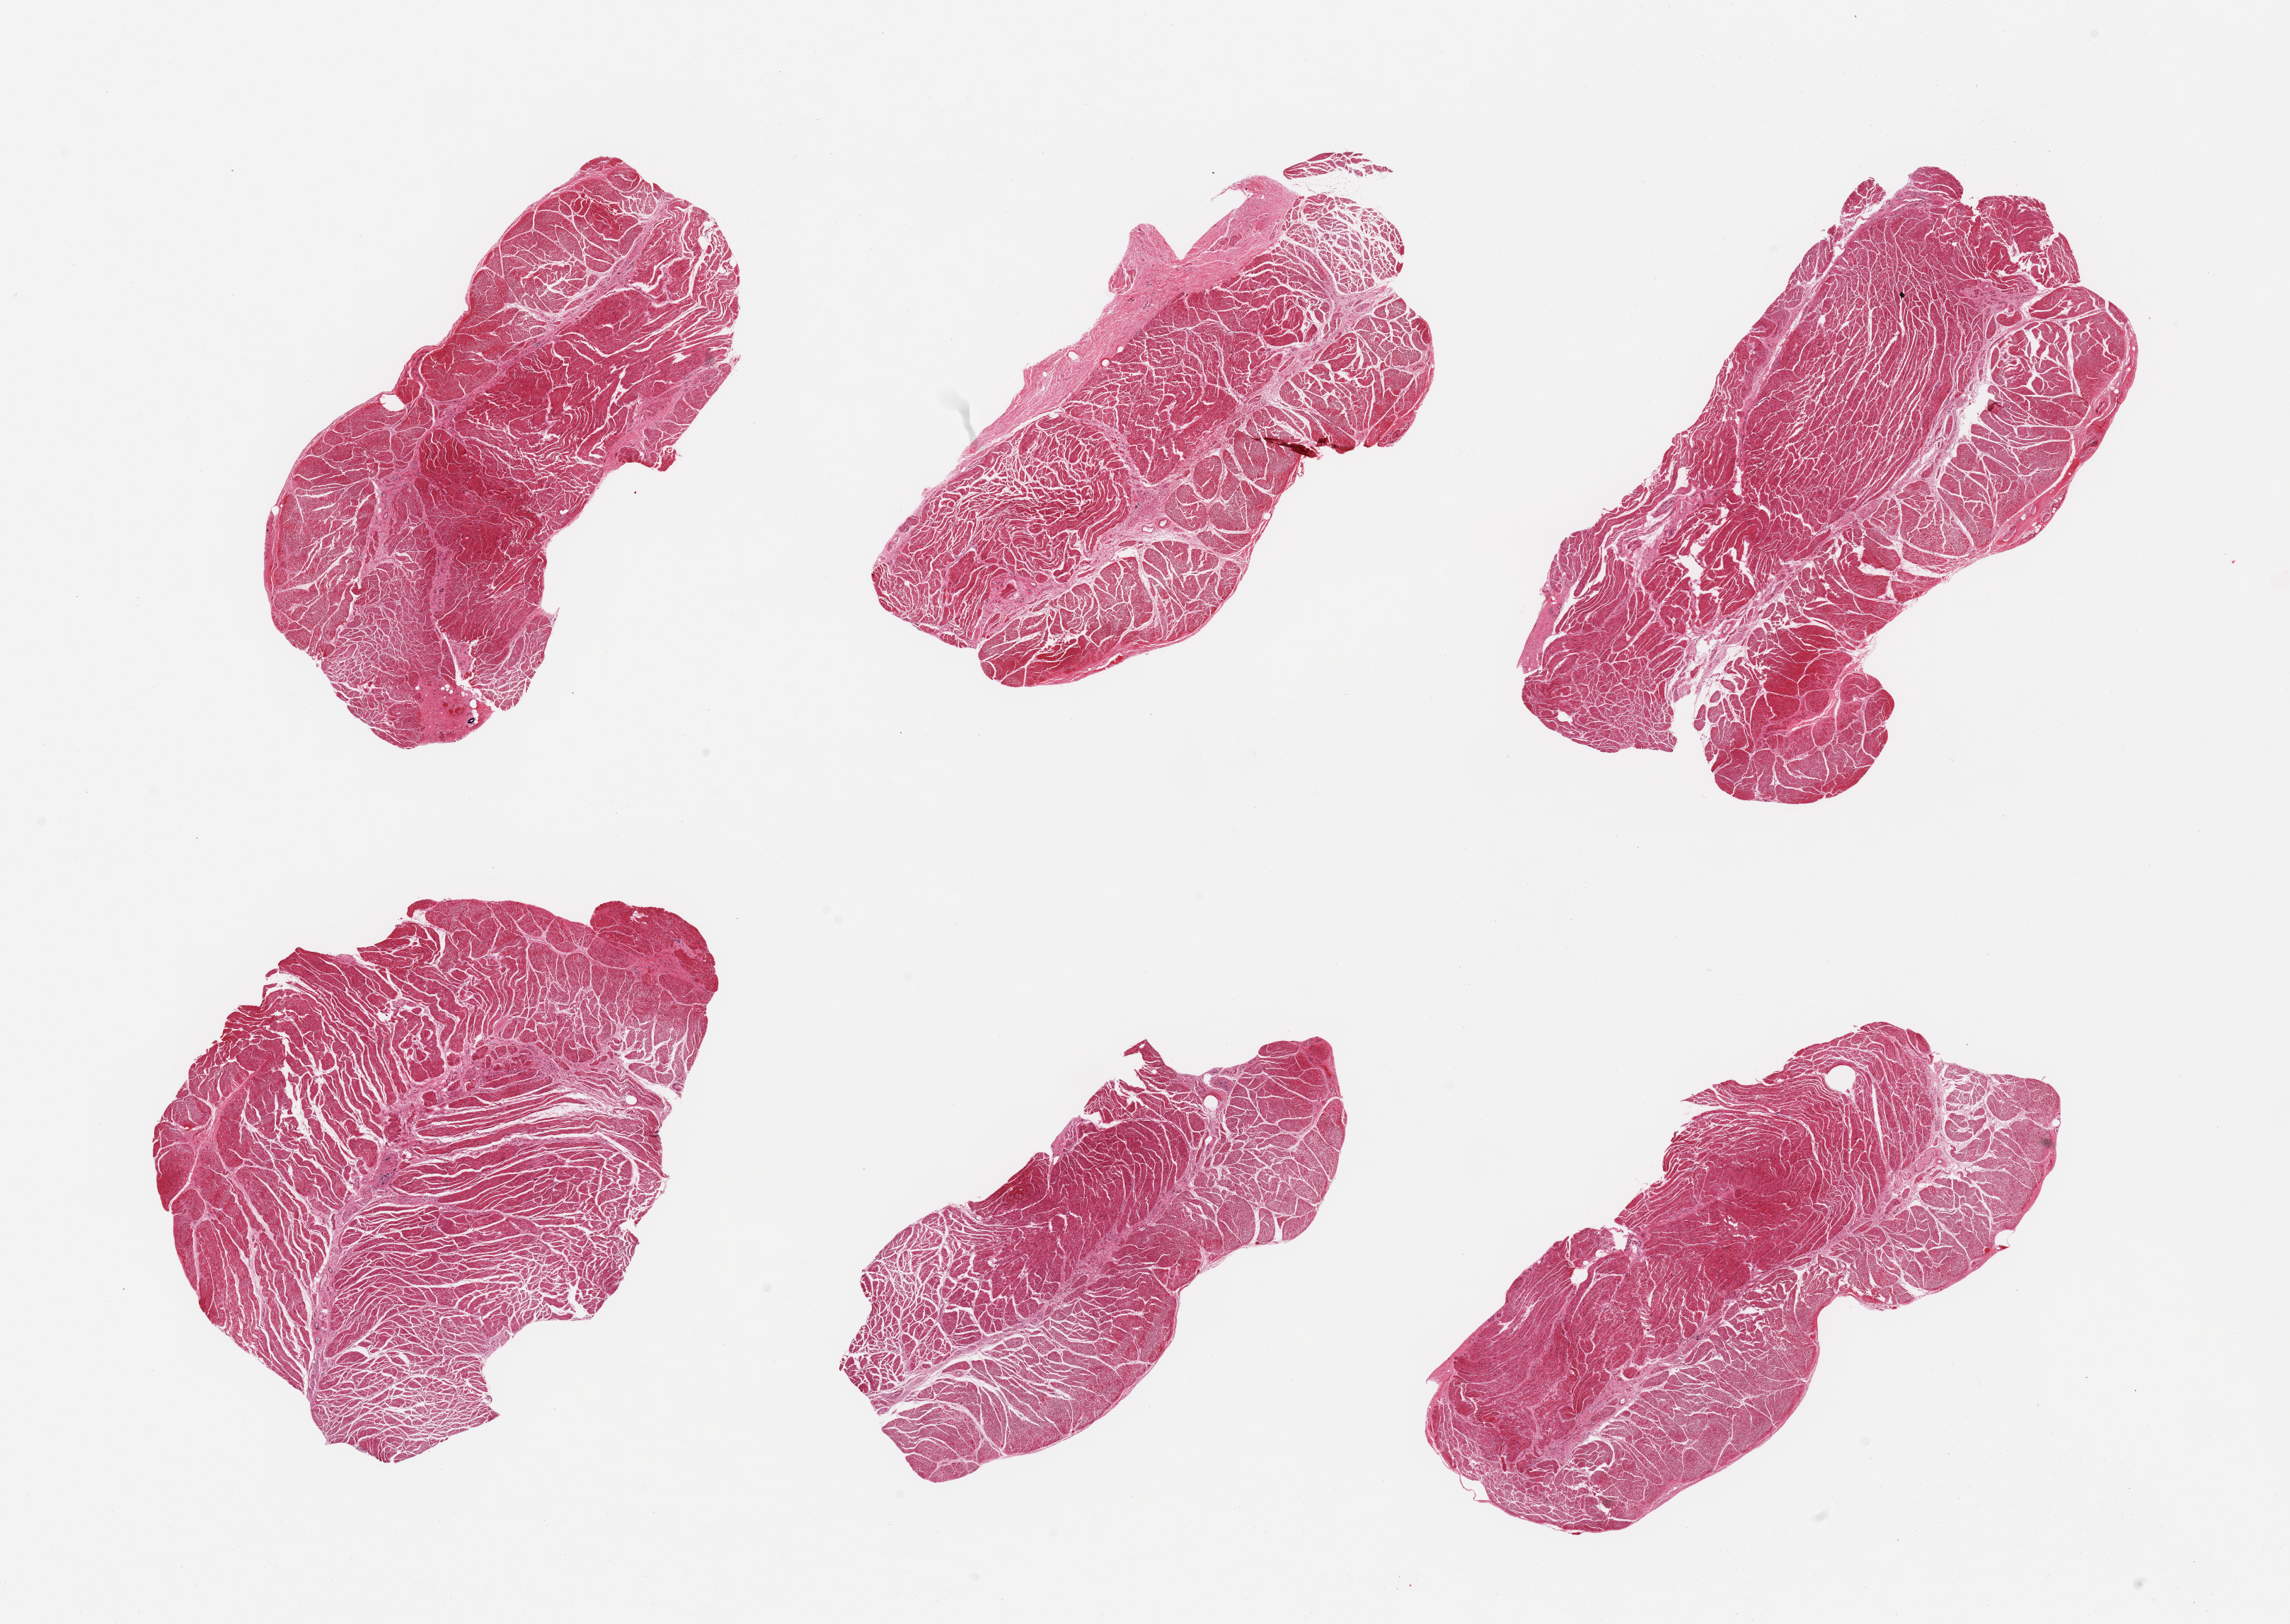
H&E whole-slide image, brightfield, a low-resolution overview of the entire scanned area, about 25.6 x 18.2 mm (from a 20x scan). PAXgene-fixed, paraffin-embedded tissue. Target tissue: gastroesophageal junction. Donor tissue sample. Male donor.
Pathologist's review note for this sample: 6 pieces, confirmed target muscularis.